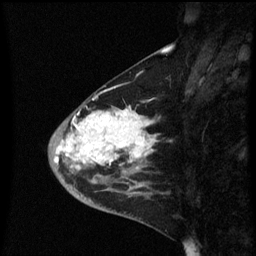
Breast MRI (dynamic contrast-enhanced), one sagittal slice; slice 23 of 60 in the series (ordered by position); dynamic contrast-enhanced series, image 2 of 3 at this slice position (ordered by acquisition); 1.5 T; TE 4.2 ms, TR 8.4 ms; 2.3 mm slice thickness; 256 × 256 image matrix, field of view 200 × 200 mm. Patient: female, 46 years. From the clinical record (not read from this slice): setting: breast cancer imaged before/during neoadjuvant chemotherapy; receptor status: HER2-positive.
Outlined on this slice (semi-automatic segmentation, software-assisted and operator-edited):
- analysis volume of interest (the breast-tissue region the enhancement analysis was run in; not a lesion): bounding box (x1, y1, x2, y2) in pixels: (48, 96, 159, 187)
- tumour enhancement mask (voxels above the 70 % enhancement threshold inside the analysis volume of interest): (54, 108, 156, 165)